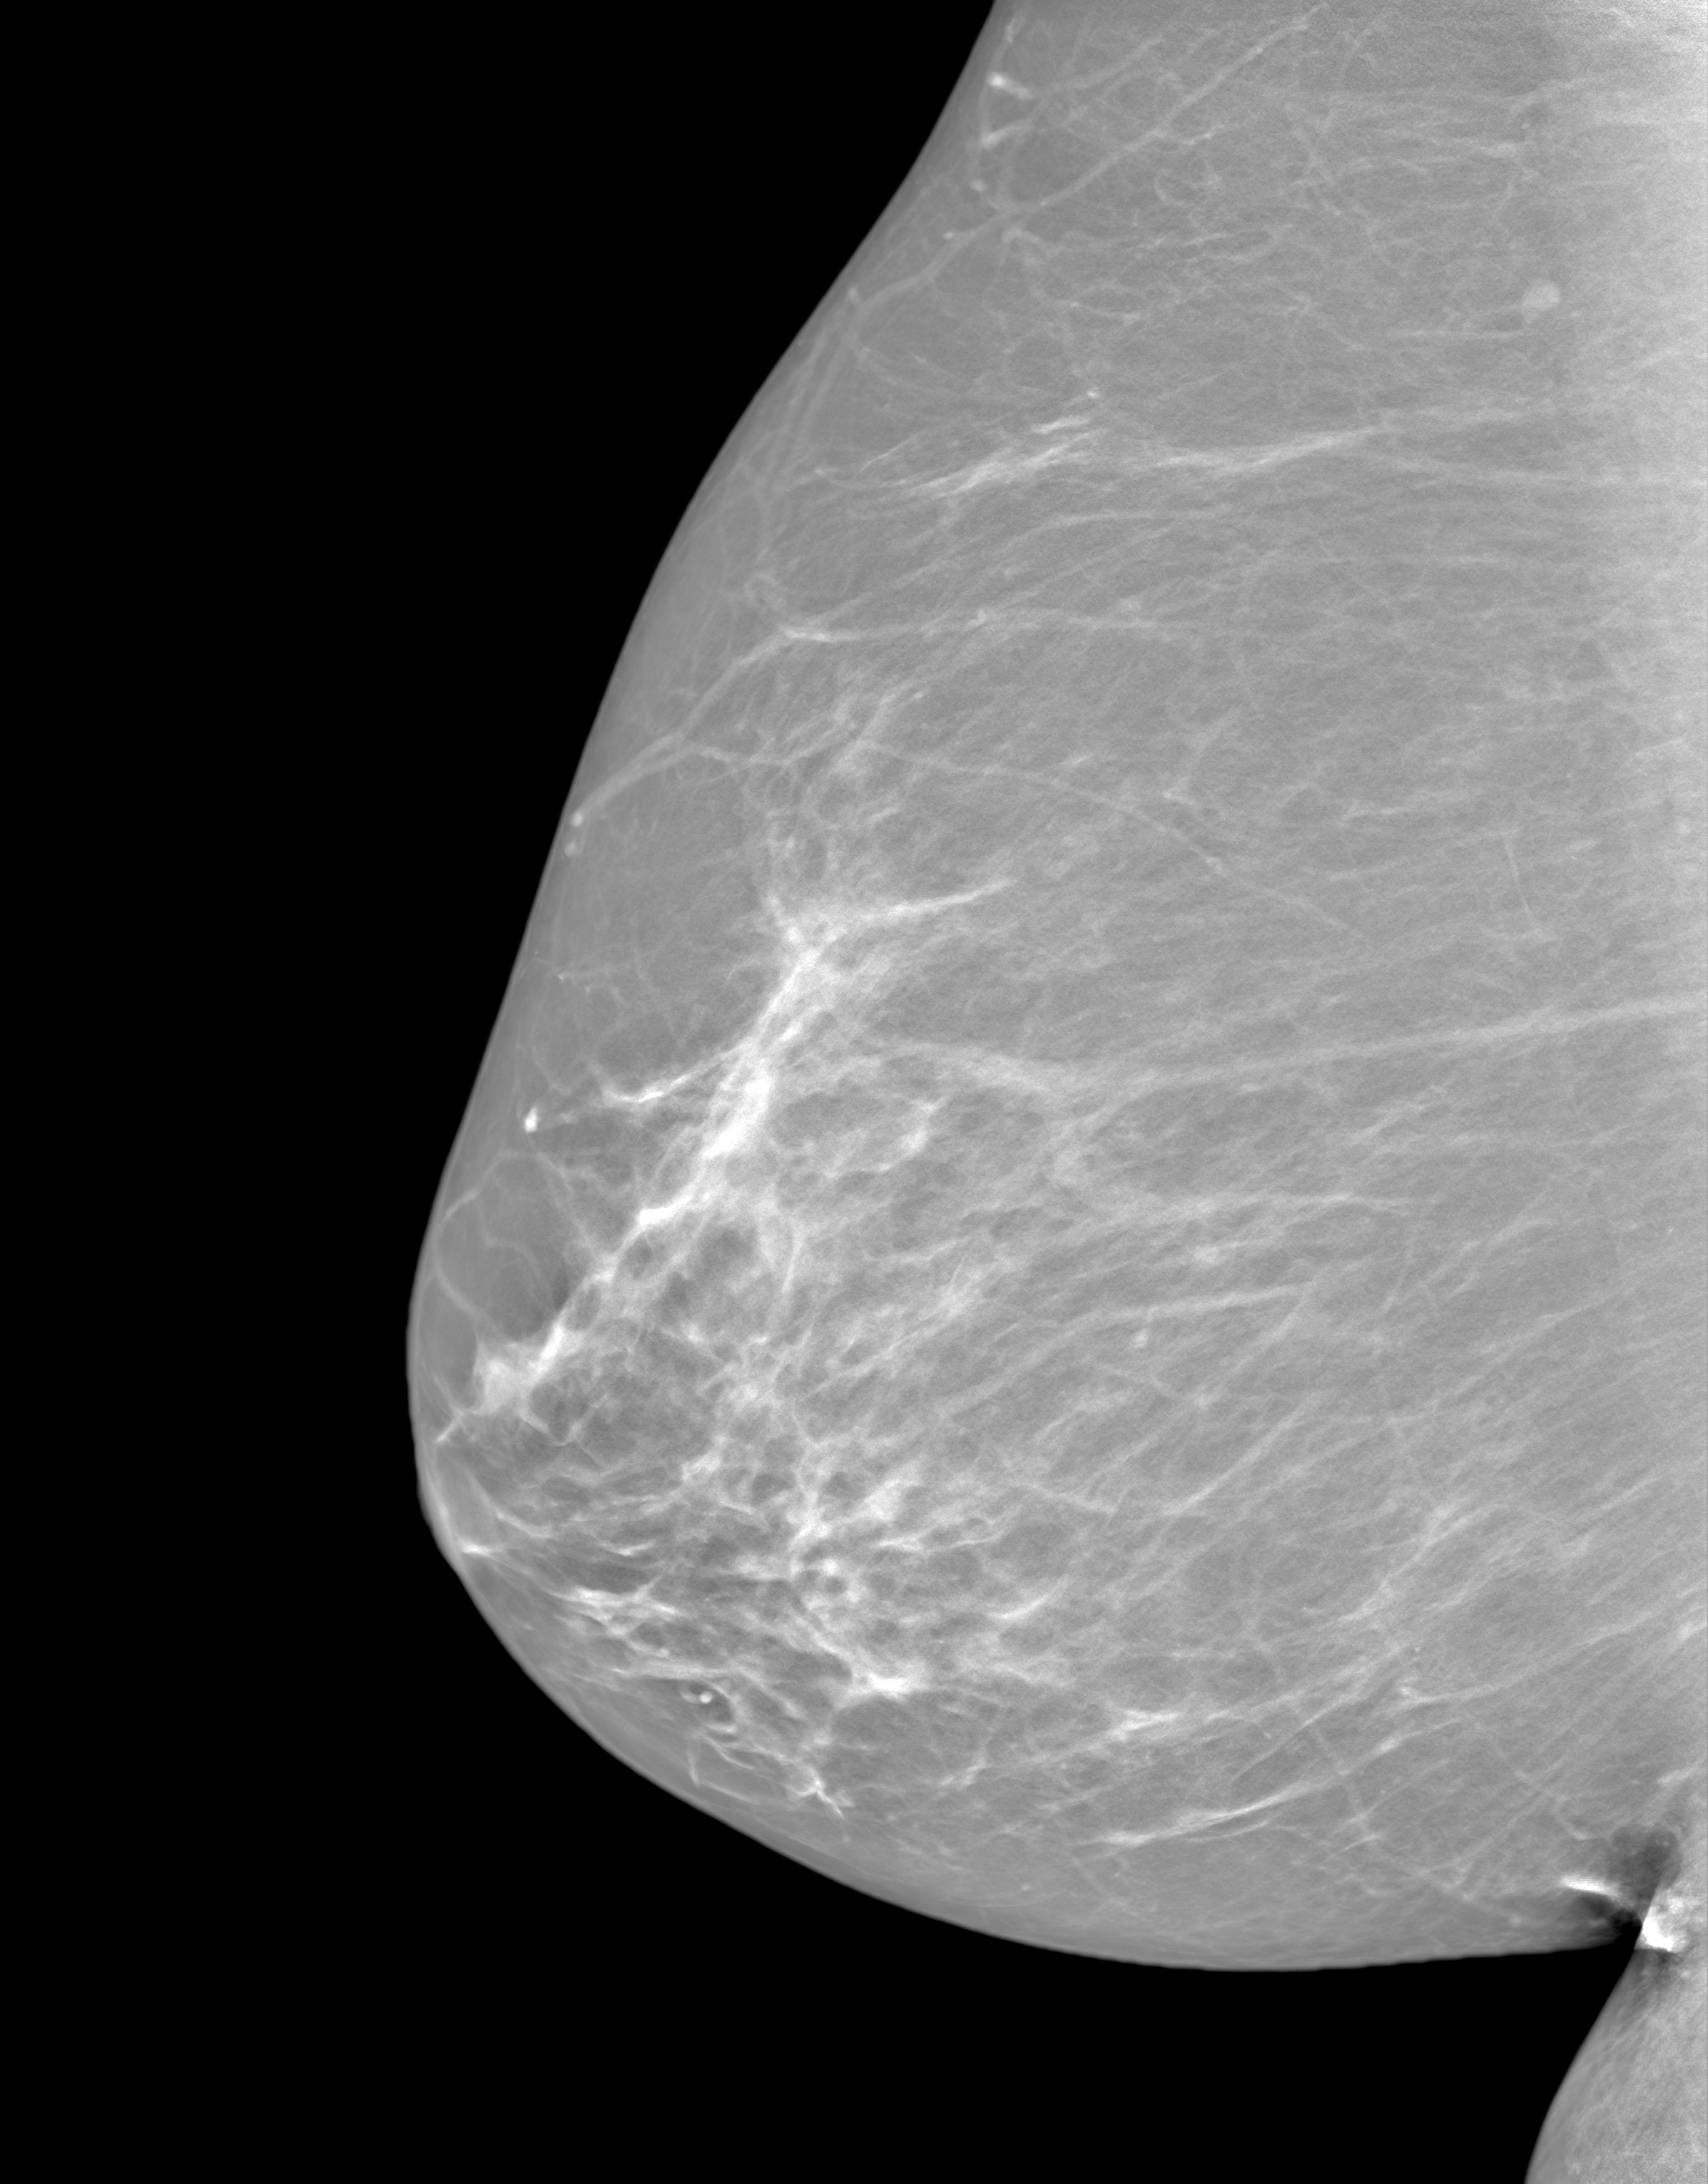
Screening examination. Female patient, age 58 years.
Image type: synthesized 2-D view from tomosynthesis. Breast: right. Projection: MLO view.